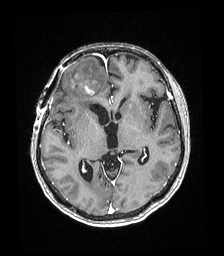
Brain MRI from a brain-tumour surgery series, one axial slice; slice 104 of 192 in the series (ordered by position); T1-weighted post-contrast; 1 mm slice thickness; 224 × 256 image matrix, field of view 219 × 250 mm. From the clinical record (not read from this slice): histopathology: Astrocytoma; WHO grade: 4; IDH mutation: yes.
Outlined on this slice (outlined manually by an expert reader):
- tumour: box from (x=86, y=89) to (x=92, y=94) px